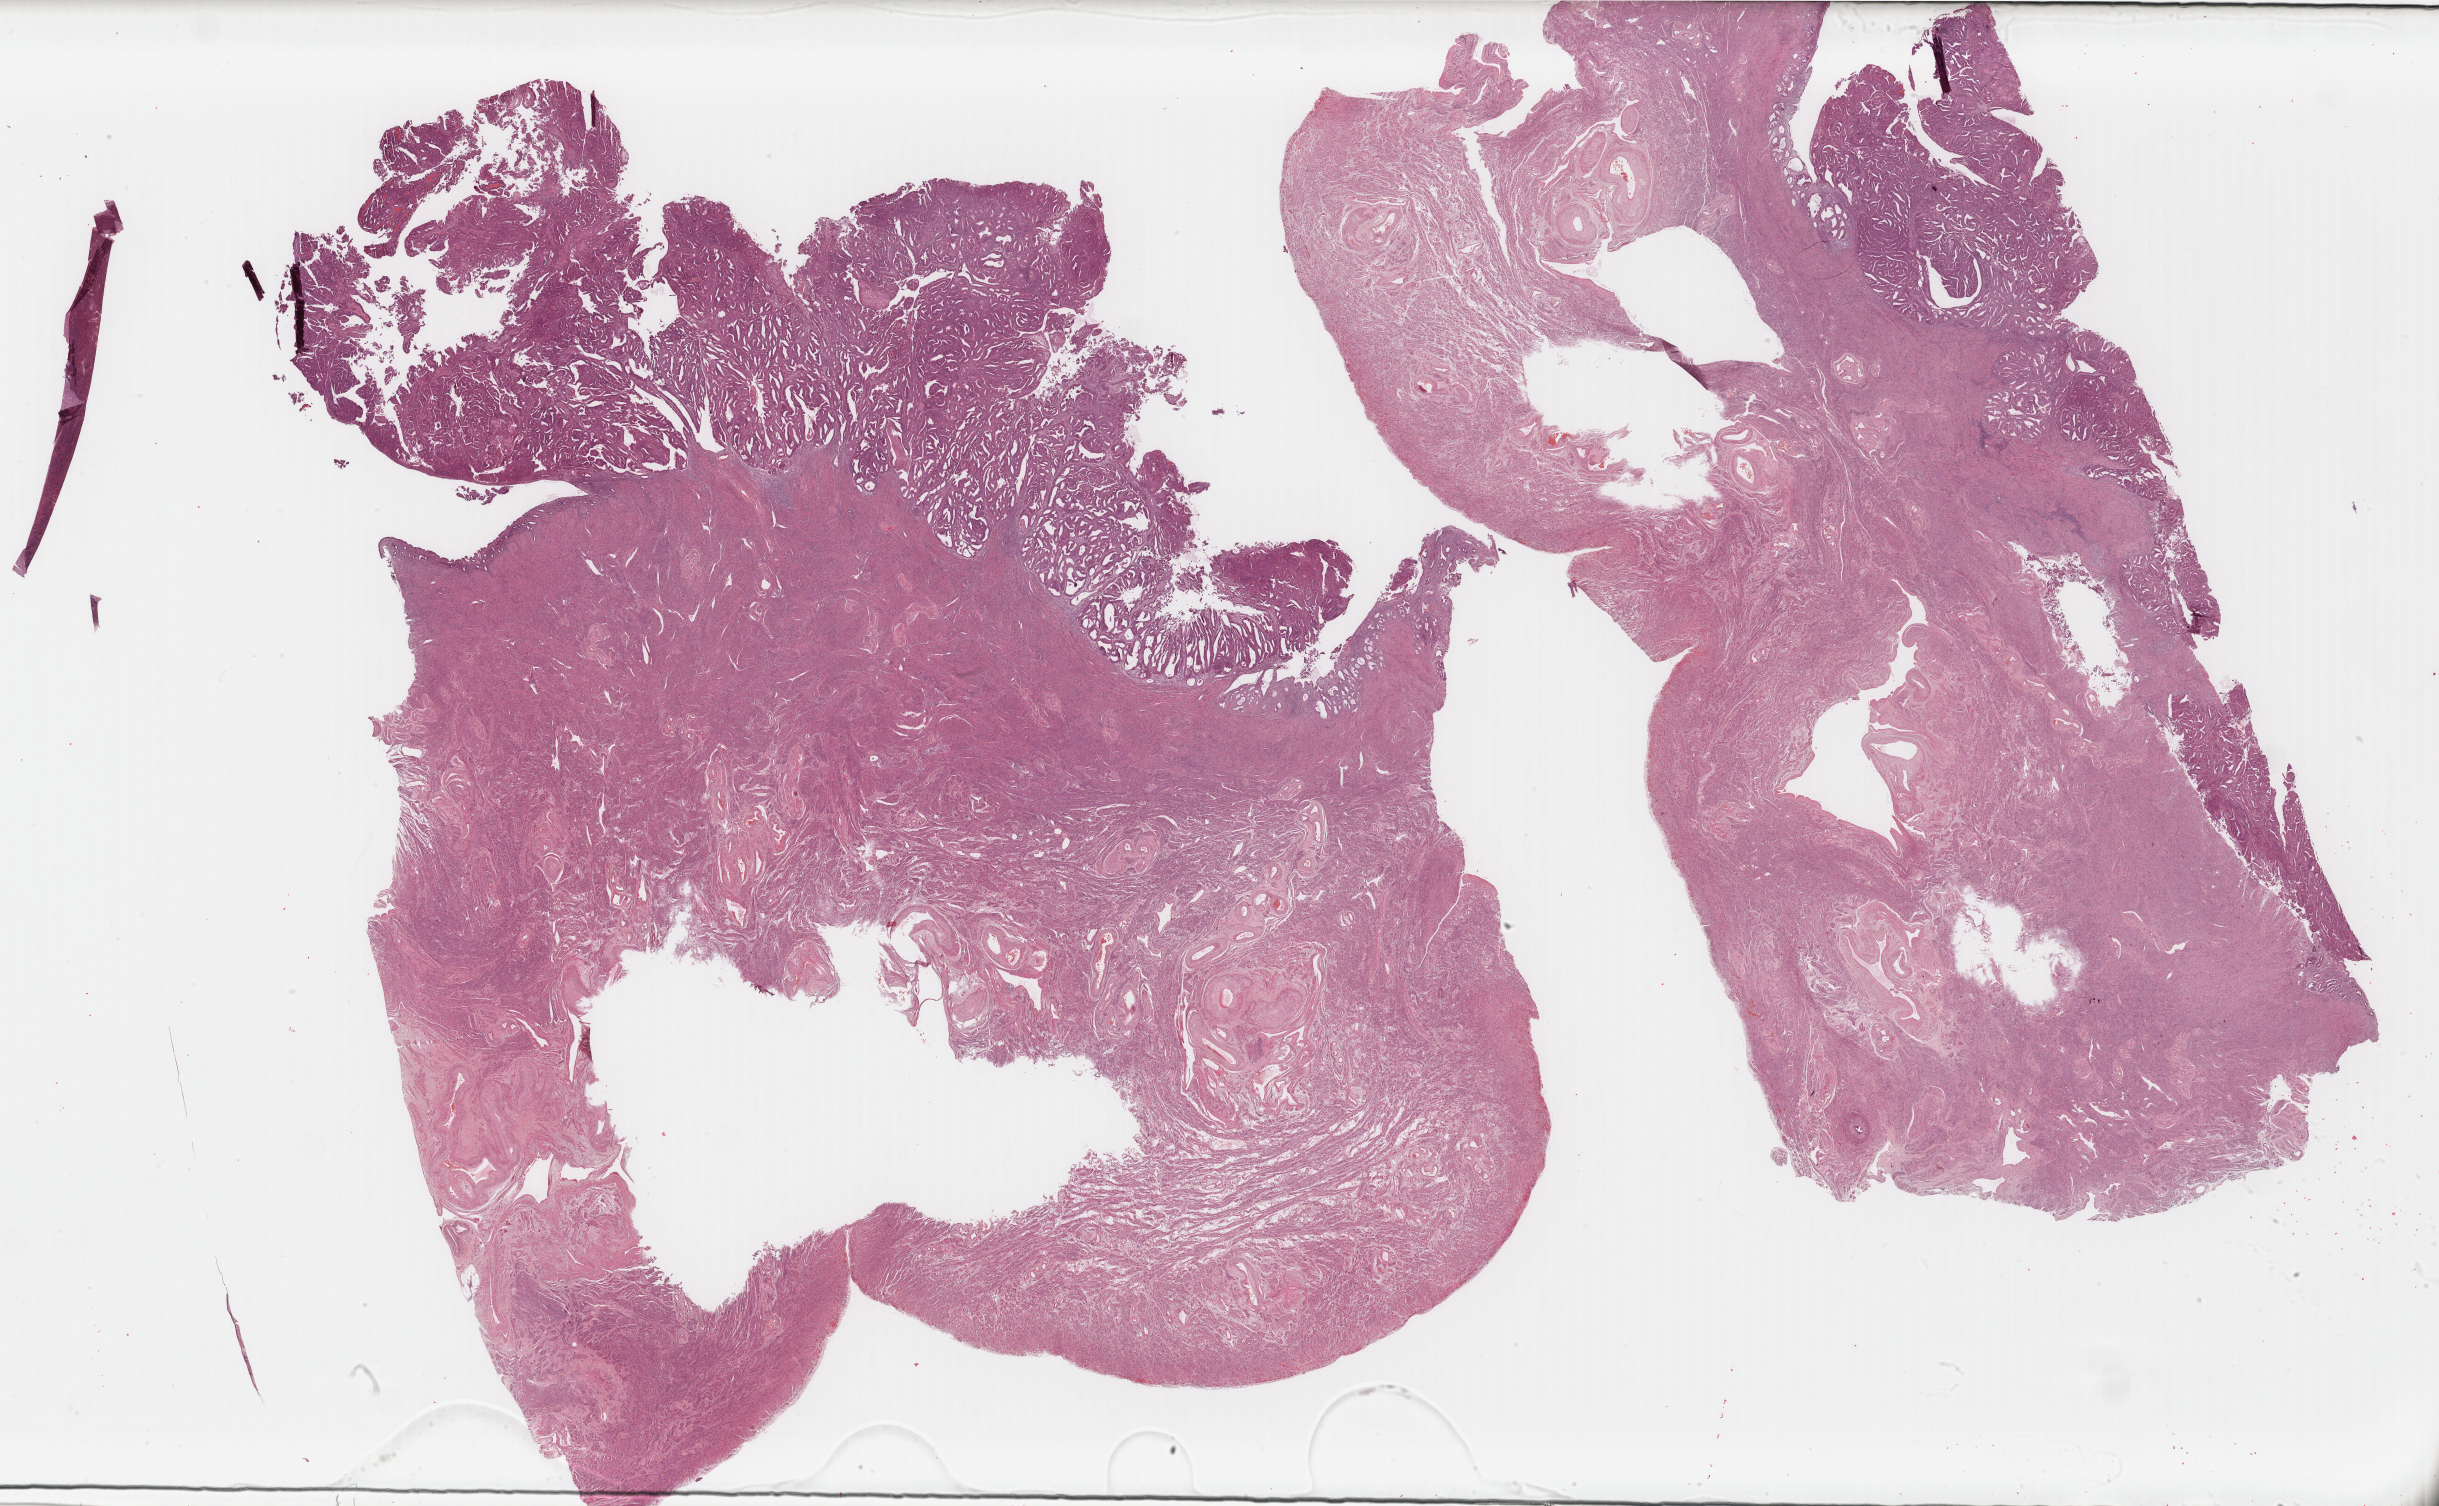
H&E-stained whole-slide image — a low-resolution overview of the entire scanned area, about 38.7 x 23.9 mm (from a 40x scan), formalin-fixed paraffin-embedded (FFPE) diagnostic section, uterus, primary tumour sample. Female, age 68 years at initial diagnosis.
Pathologic diagnosis: Endometrioid adenocarcinoma, NOS (endometrium).